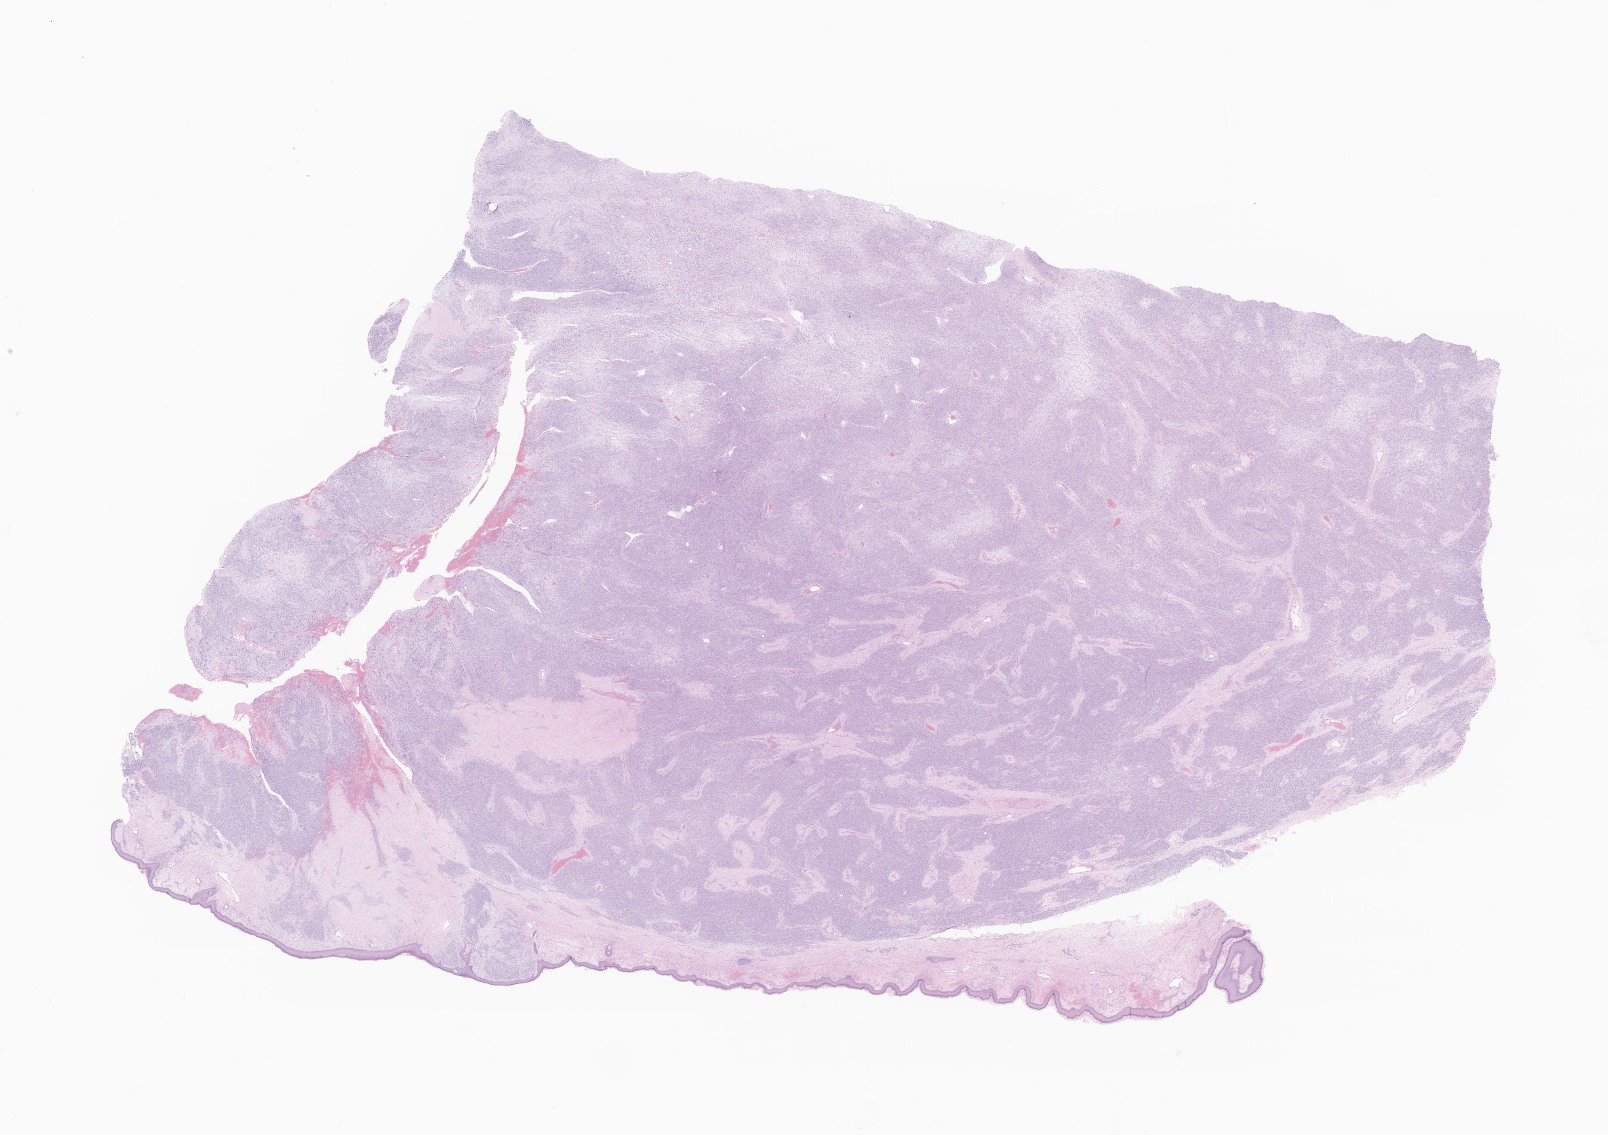
Whole-slide image, H&E stain of tumor tissue from the orbit, shown as a low-resolution overview of the whole scanned area (about 27.1 x 19.1 mm); formalin-fixed, paraffin-embedded (FFPE) tissue. Patient female; age 116 months (9 years 8 months).
Diagnosis (ICD-O-3 morphology term): Tumor cells, uncertain whether benign or malignant.